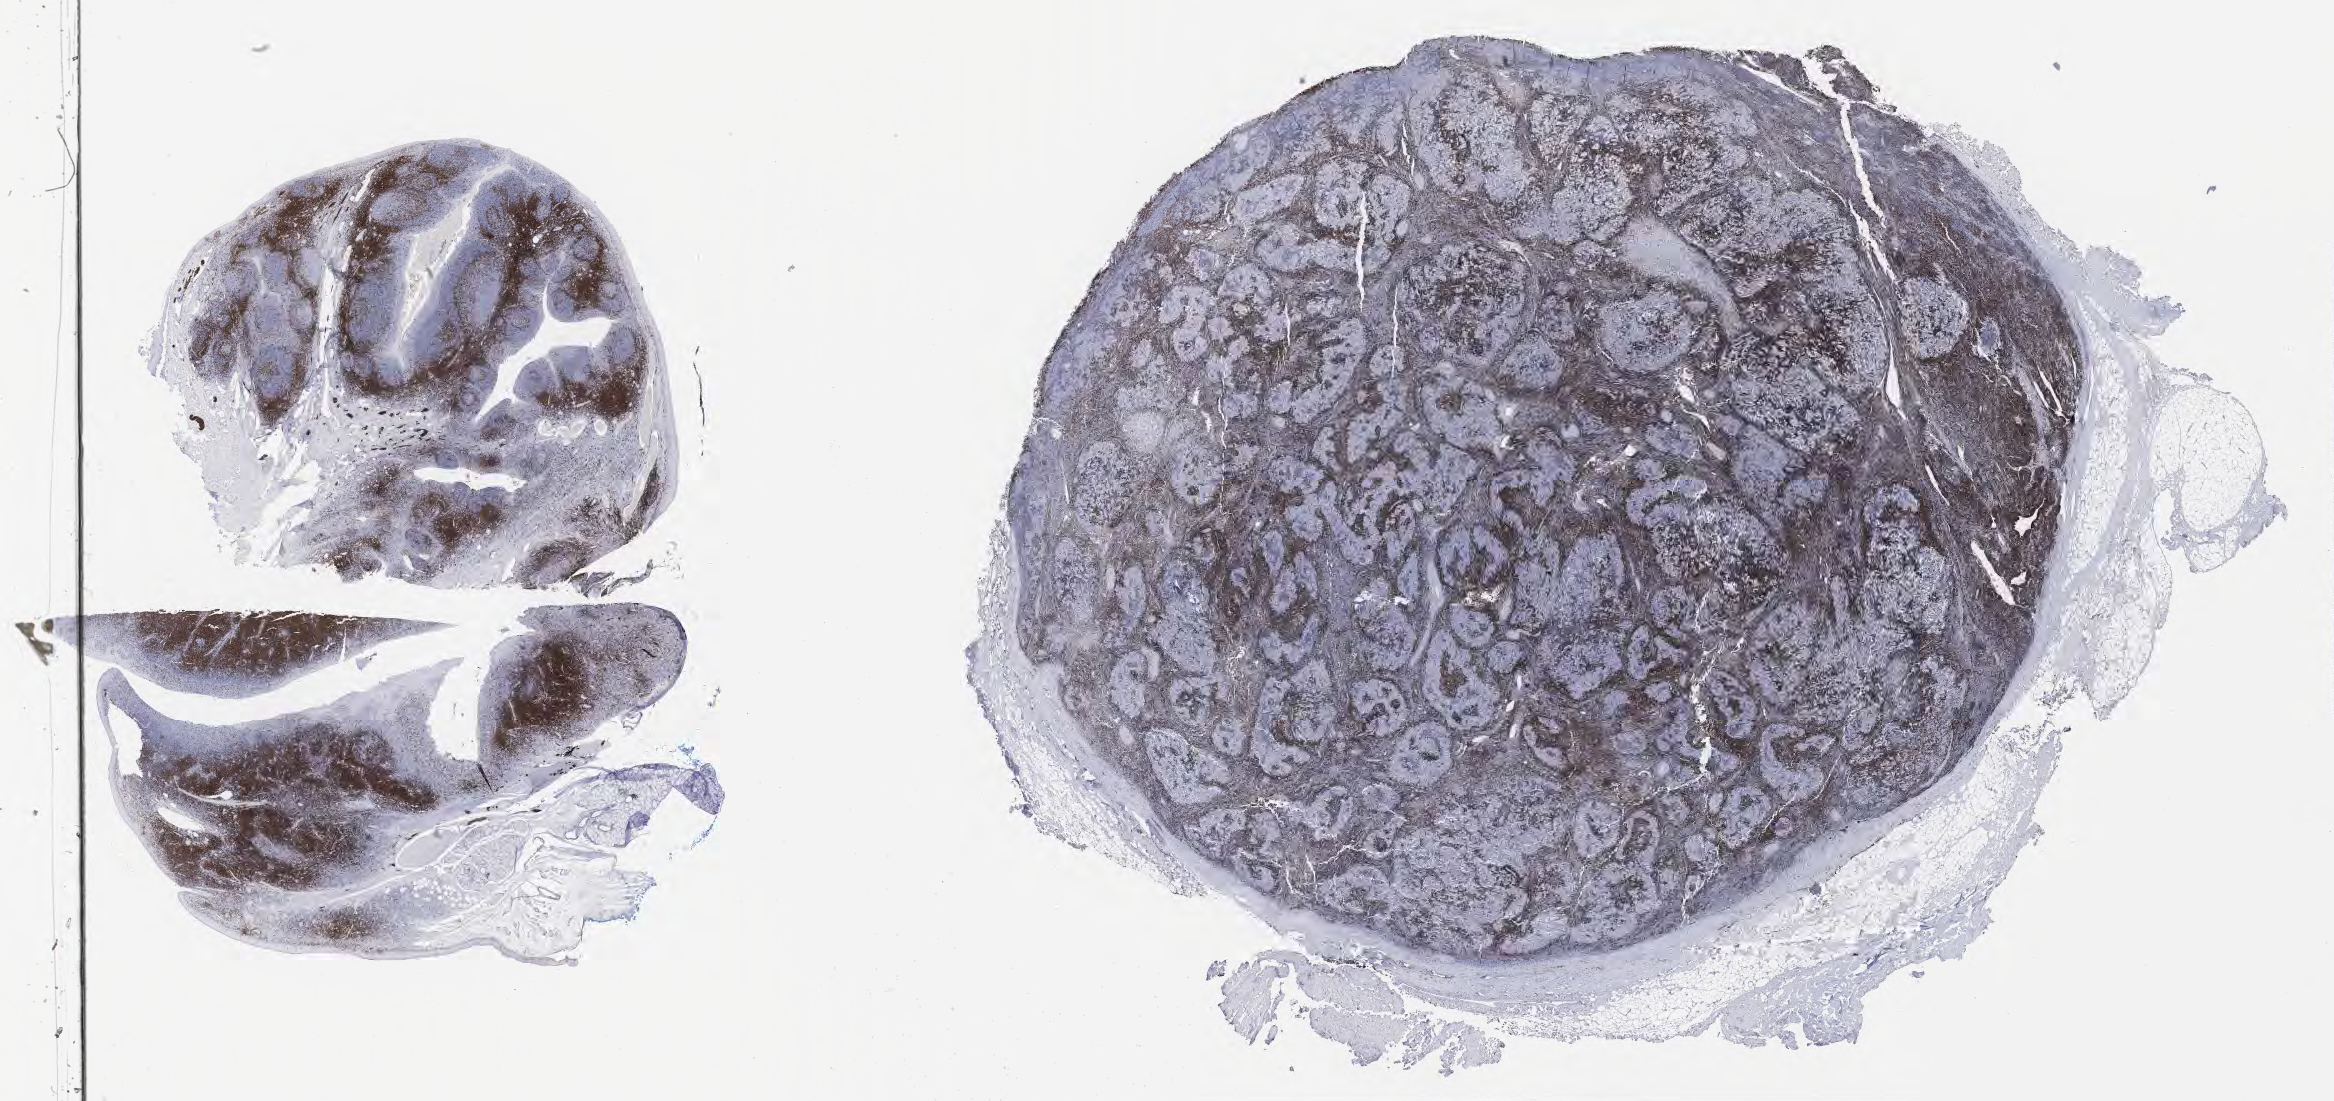
IHC for CD3, whole-slide image — shown as a low-resolution overview of the whole scanned area (about 37.7 x 17.8 mm); specimen: tumor tissue; anatomic site: lymph node. Male patient, aged 46.
• histologic diagnosis: Diffuse large B-cell lymphoma, NOS